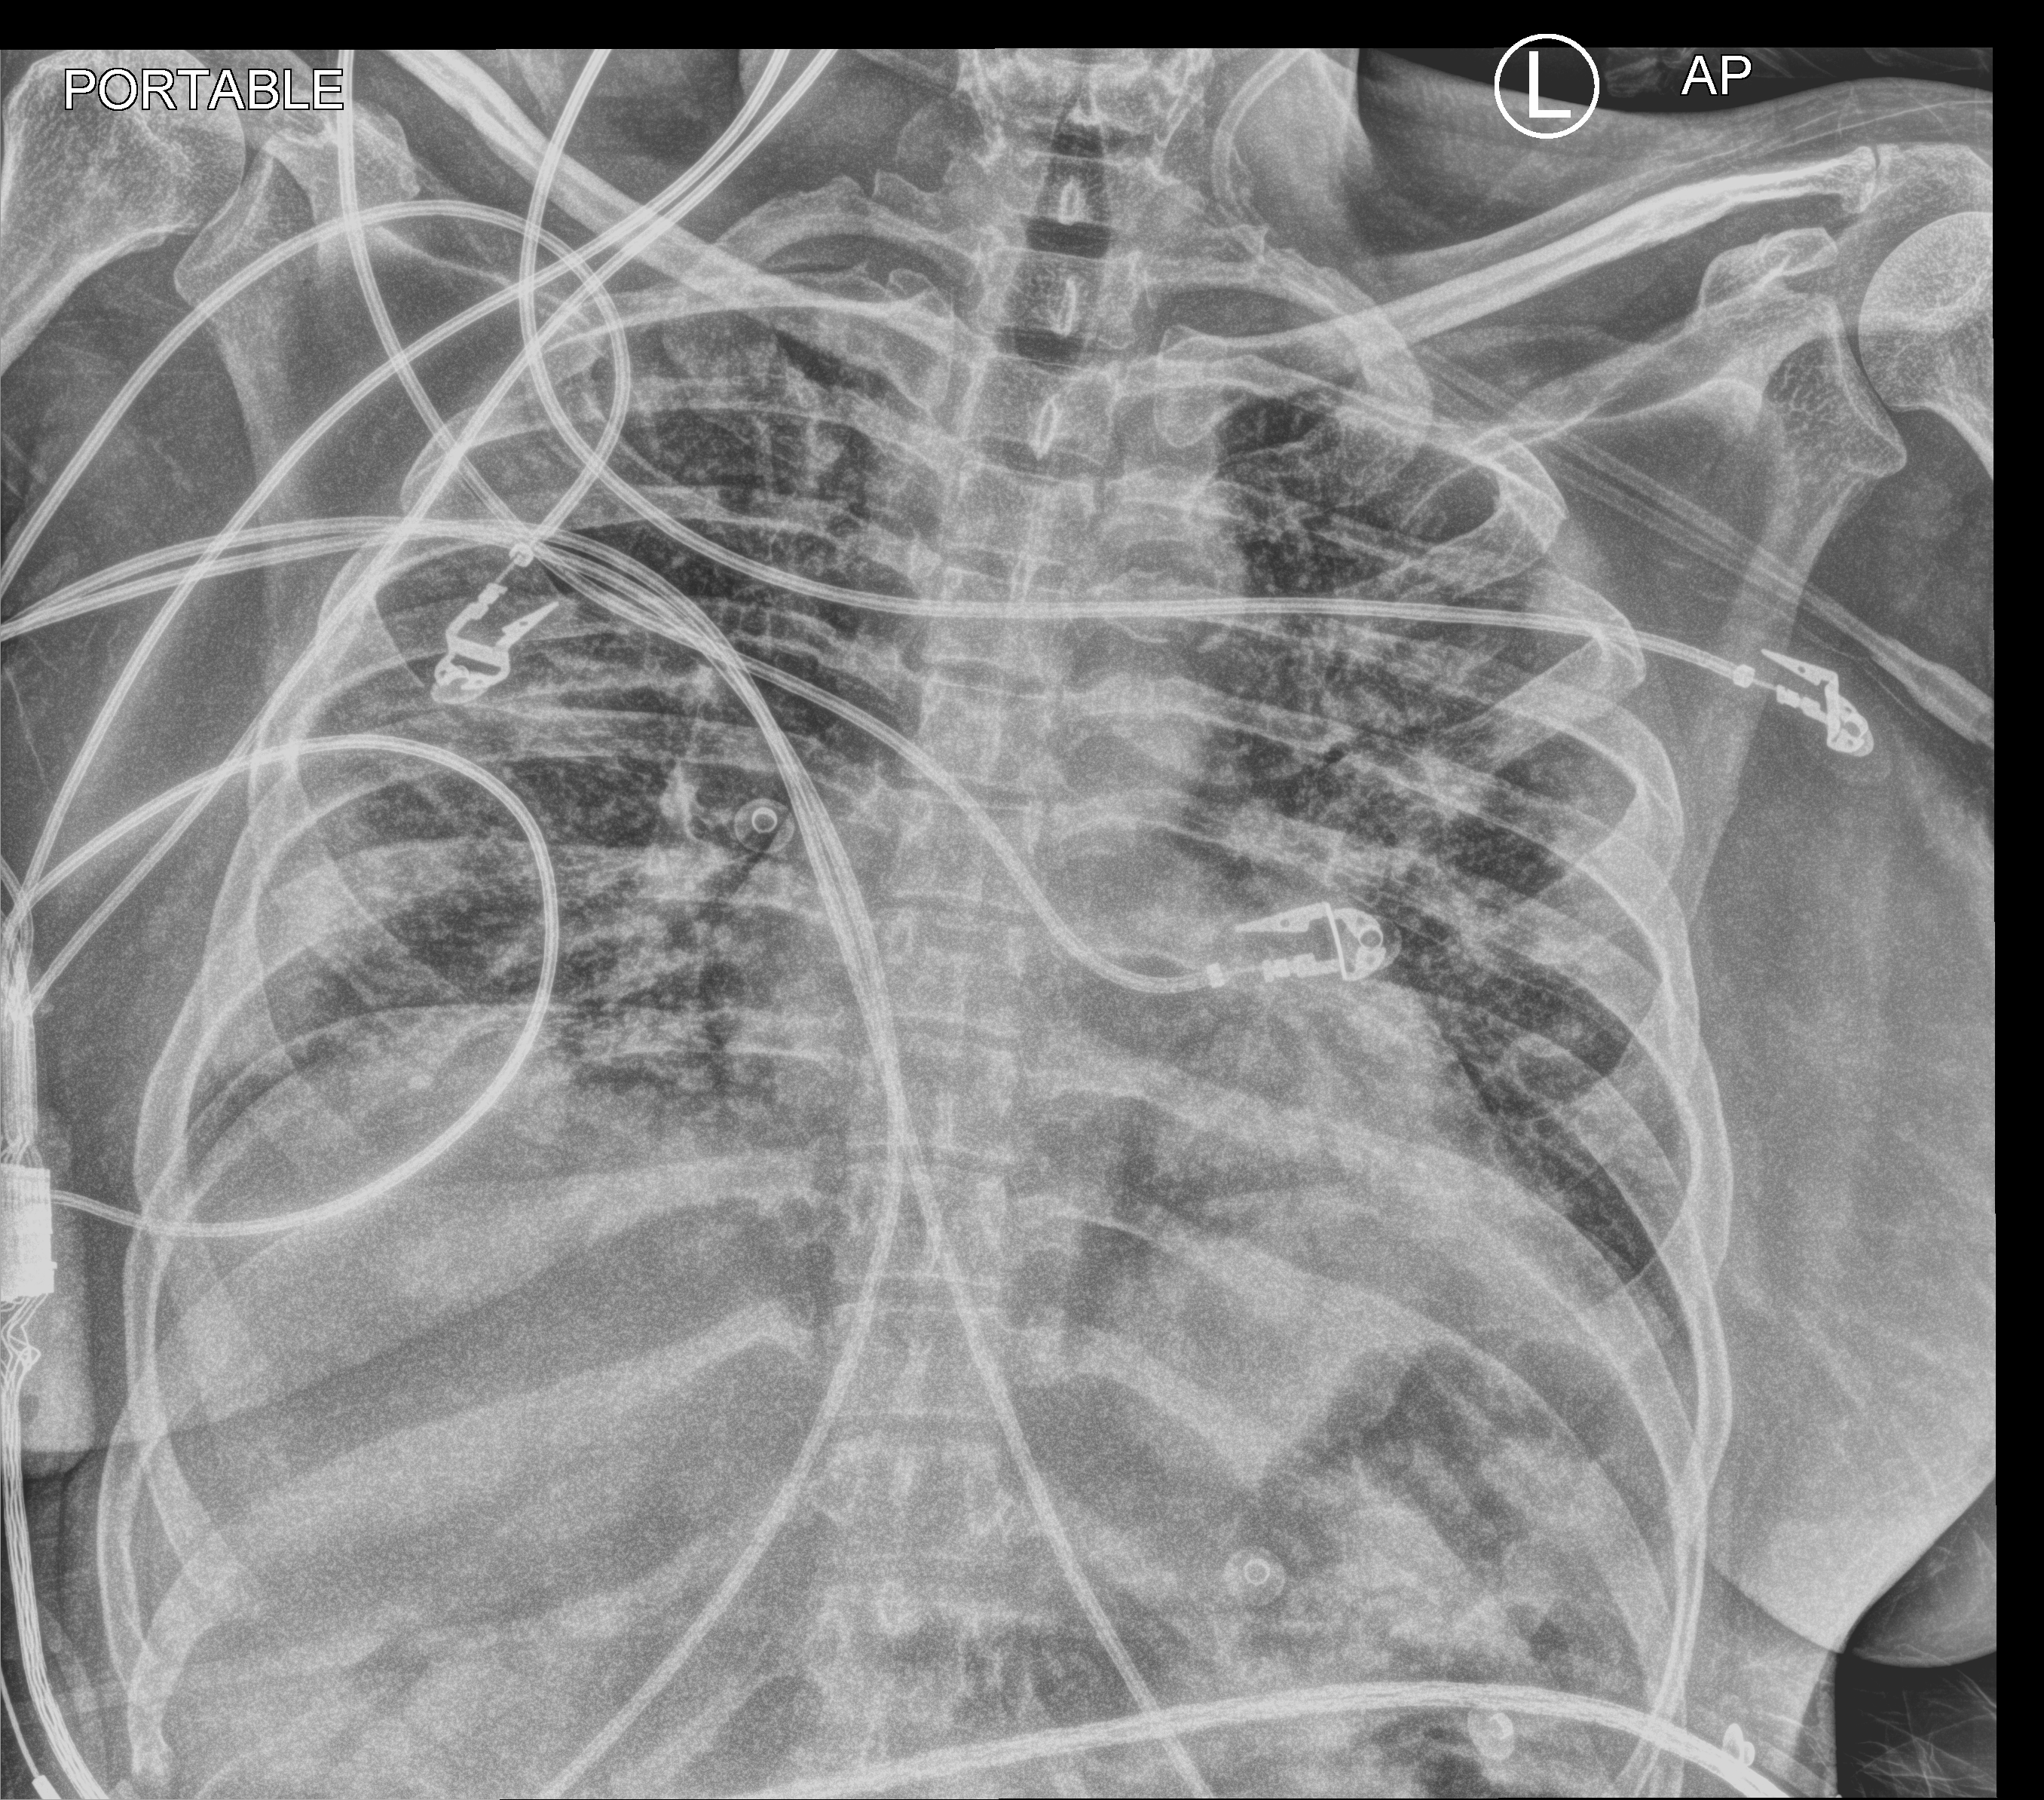
Chest X-ray (portable), anteroposterior (AP) projection. Patient hospitalised with COVID-19, aged 18–59 years.
Admission-level facts for this patient (not findings on this image; timing relative to this image not recorded): admitted to intensive care during this hospital stay: yes; mechanically ventilated during this hospital stay: yes.